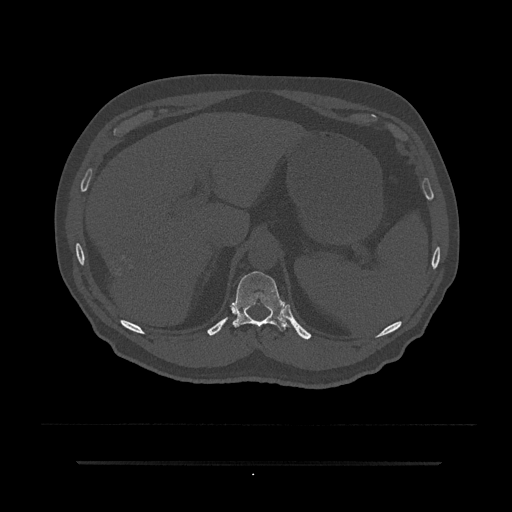
CT including the spine, one axial slice. Slice 272 of 797 in the series (ordered by position). 120 kVp. Bone window (W 1800 / L 400 HU). 0.5 mm slice thickness. 512 × 512 image matrix, field of view 464 × 464 mm. Patient: male, 59 years. Case-level facts recorded for this patient, not image findings: primary cancer: bile ducts; vertebrae with lytic lesions (as recorded): T10.
Structures marked on this image (semi-automatically segmented with operator editing):
- T11 vertebra: box from (x=232, y=271) to (x=296, y=331) px